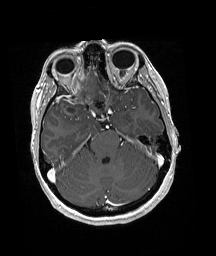
Brain MRI from a brain-tumour surgery series, one axial slice; T1-weighted post-contrast; 1 mm slice thickness; 216 × 256 image matrix, field of view 211 × 250 mm. Case-level facts recorded for this patient, not image findings: histopathology: Oligodendroglioma; WHO grade: 3; IDH mutation: yes.
Outlined on this slice (manually delineated by an expert):
- tumour: bounding box <54,73,97,114> (left, top, right, bottom; pixels)